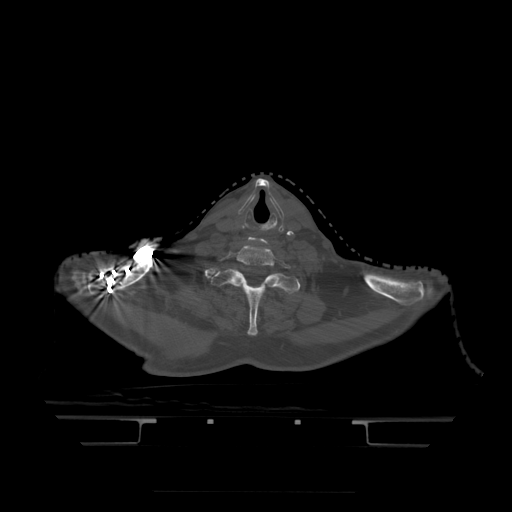
CT including the spine, one axial slice; slice 405 of 522 in the series (ordered by position); bone window (W 1800 / L 400 HU); 512 × 512 image matrix, field of view 436 × 436 mm. Patient age 68 years. From the clinical record (not read from this slice): primary cancer: urothelial.
Annotated regions visible in this slice (semi-automatically segmented with operator editing):
- T1 vertebra: bounding box [x1, y1, x2, y2] px = [212, 270, 301, 336]